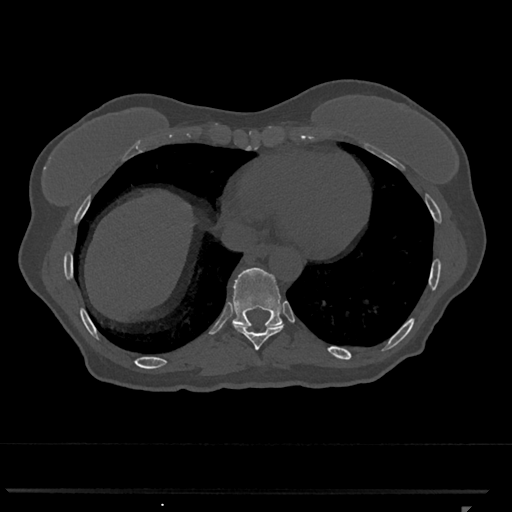
CT including the spine, one axial slice. Position 597 of 793 along the scan axis. Bone window (W 1800 / L 400 HU). 0.5 mm slice thickness. 512 × 512 image matrix, field of view 380 × 380 mm. Female patient, age 62 years. Case-level facts recorded for this patient, not image findings: primary cancer: renal.
Annotated regions visible in this slice (semi-automatic segmentation, software-assisted and operator-edited):
- T10 vertebra: bounding box <232,267,283,327> (left, top, right, bottom; pixels)
- T9 vertebra: <233,323,284,350>